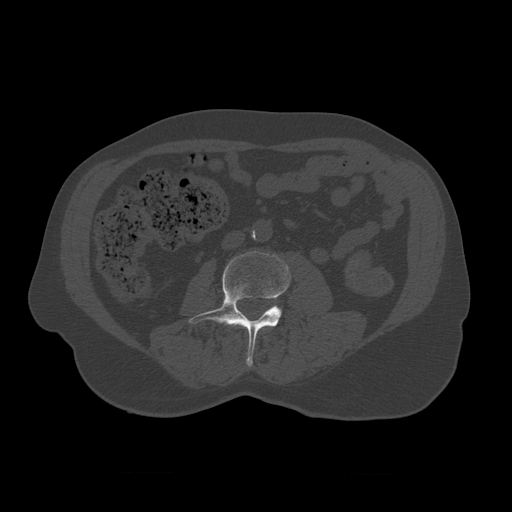
CT including the spine, one axial slice. Slice 302 of 450 in the series (ordered by position). Reconstruction kernel STANDARD. 120 kVp. Bone window (W 1800 / L 400 HU). 1.25 mm slice thickness. 512 × 512 image matrix, field of view 405 × 405 mm. Patient age 75 years. From the clinical record (not read from this slice): primary cancer: prostate.
Annotated regions visible in this slice (semi-automatically segmented with operator editing):
- L3 vertebra: bounding box (x1, y1, x2, y2) in pixels: (189, 251, 292, 368)